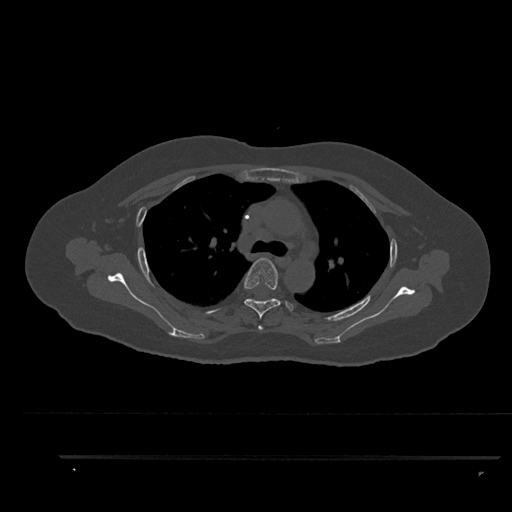
CT including the spine, one axial slice. Position 640 of 797 along the scan axis. 120 kVp. Bone window (W 1800 / L 400 HU). 0.5 mm slice thickness. 512 × 512 image matrix, field of view 408 × 408 mm. Female patient, age 44 years. Case-level facts recorded for this patient, not image findings: primary cancer: renal.
Annotated regions visible in this slice (semi-automatically segmented with operator editing):
- T3 vertebra: box from (x=258, y=325) to (x=264, y=331) px
- T4 vertebra: (x=244, y=258)–(x=294, y=319)